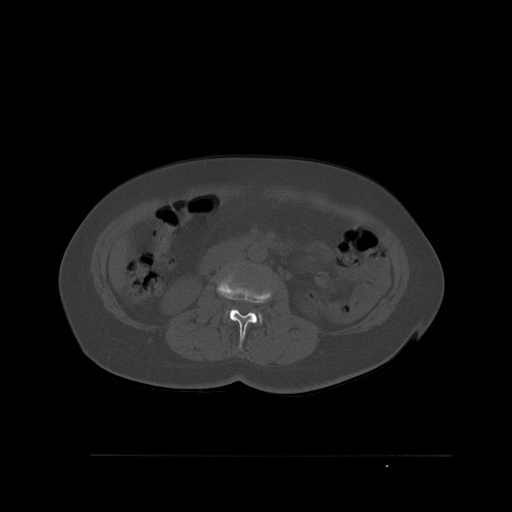
CT including the spine, one axial slice. Position 241 of 527 along the scan axis. Bone window (W 1800 / L 400 HU). 512 × 512 image matrix, field of view 470 × 470 mm. Female patient, age 73 years. From the clinical record (not read from this slice): primary cancer: breast.
Annotated regions visible in this slice (semi-automatically segmented with operator editing):
- L2 vertebra: bounding box <220,270,269,348> (left, top, right, bottom; pixels)
- L3 vertebra: <226,309,262,323>
- L4 vertebra: <252,310,255,312>